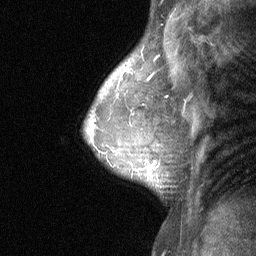
Breast MRI (dynamic contrast-enhanced), one sagittal slice; slice 47 of 64 in the series (ordered by position); dynamic contrast-enhanced study with each time point stored as its own series, time point 2 of 3 at this slice position (early post-contrast, ordered by acquisition time); 1.5 T; TE 4.8 ms, TR 27 ms; 2 mm slice thickness; 256 × 256 image matrix, field of view 180 × 180 mm. Female patient, age 47 years. From the clinical record (not read from this slice): setting: breast cancer imaged before/during neoadjuvant chemotherapy; receptor status: HR-positive, HER2-negative.
Structures marked on this image (semi-automatically segmented with operator editing):
- analysis volume of interest (the breast-tissue region the enhancement analysis was run in; not a lesion): bounding box (x1, y1, x2, y2) in pixels: (104, 138, 165, 195)
- tumour enhancement mask (voxels above the 90 % enhancement threshold inside the analysis volume of interest): (145, 159, 160, 169)